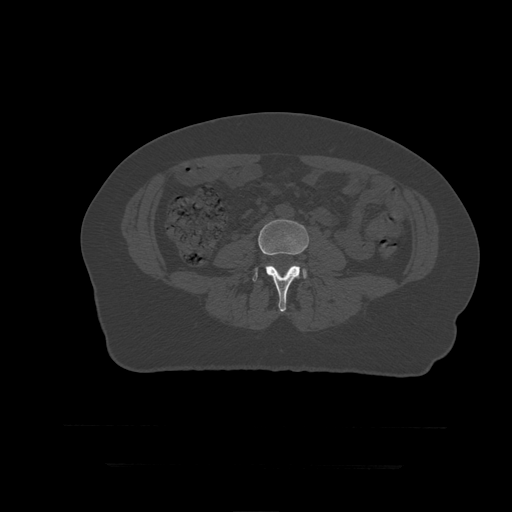
CT including the spine, one axial slice; slice 93 of 399 in the series (ordered by position); reconstruction kernel STANDARD; 120 kVp; bone window (W 1800 / L 400 HU); 512 × 512 image matrix, field of view 450 × 450 mm. Patient age 41 years. From the clinical record (not read from this slice): primary cancer: breast.
Annotated regions visible in this slice (semi-automatic segmentation, software-assisted and operator-edited):
- L4 vertebra: bounding box [x1, y1, x2, y2] px = [253, 219, 310, 312]
- L5 vertebra: [300, 269, 307, 279]